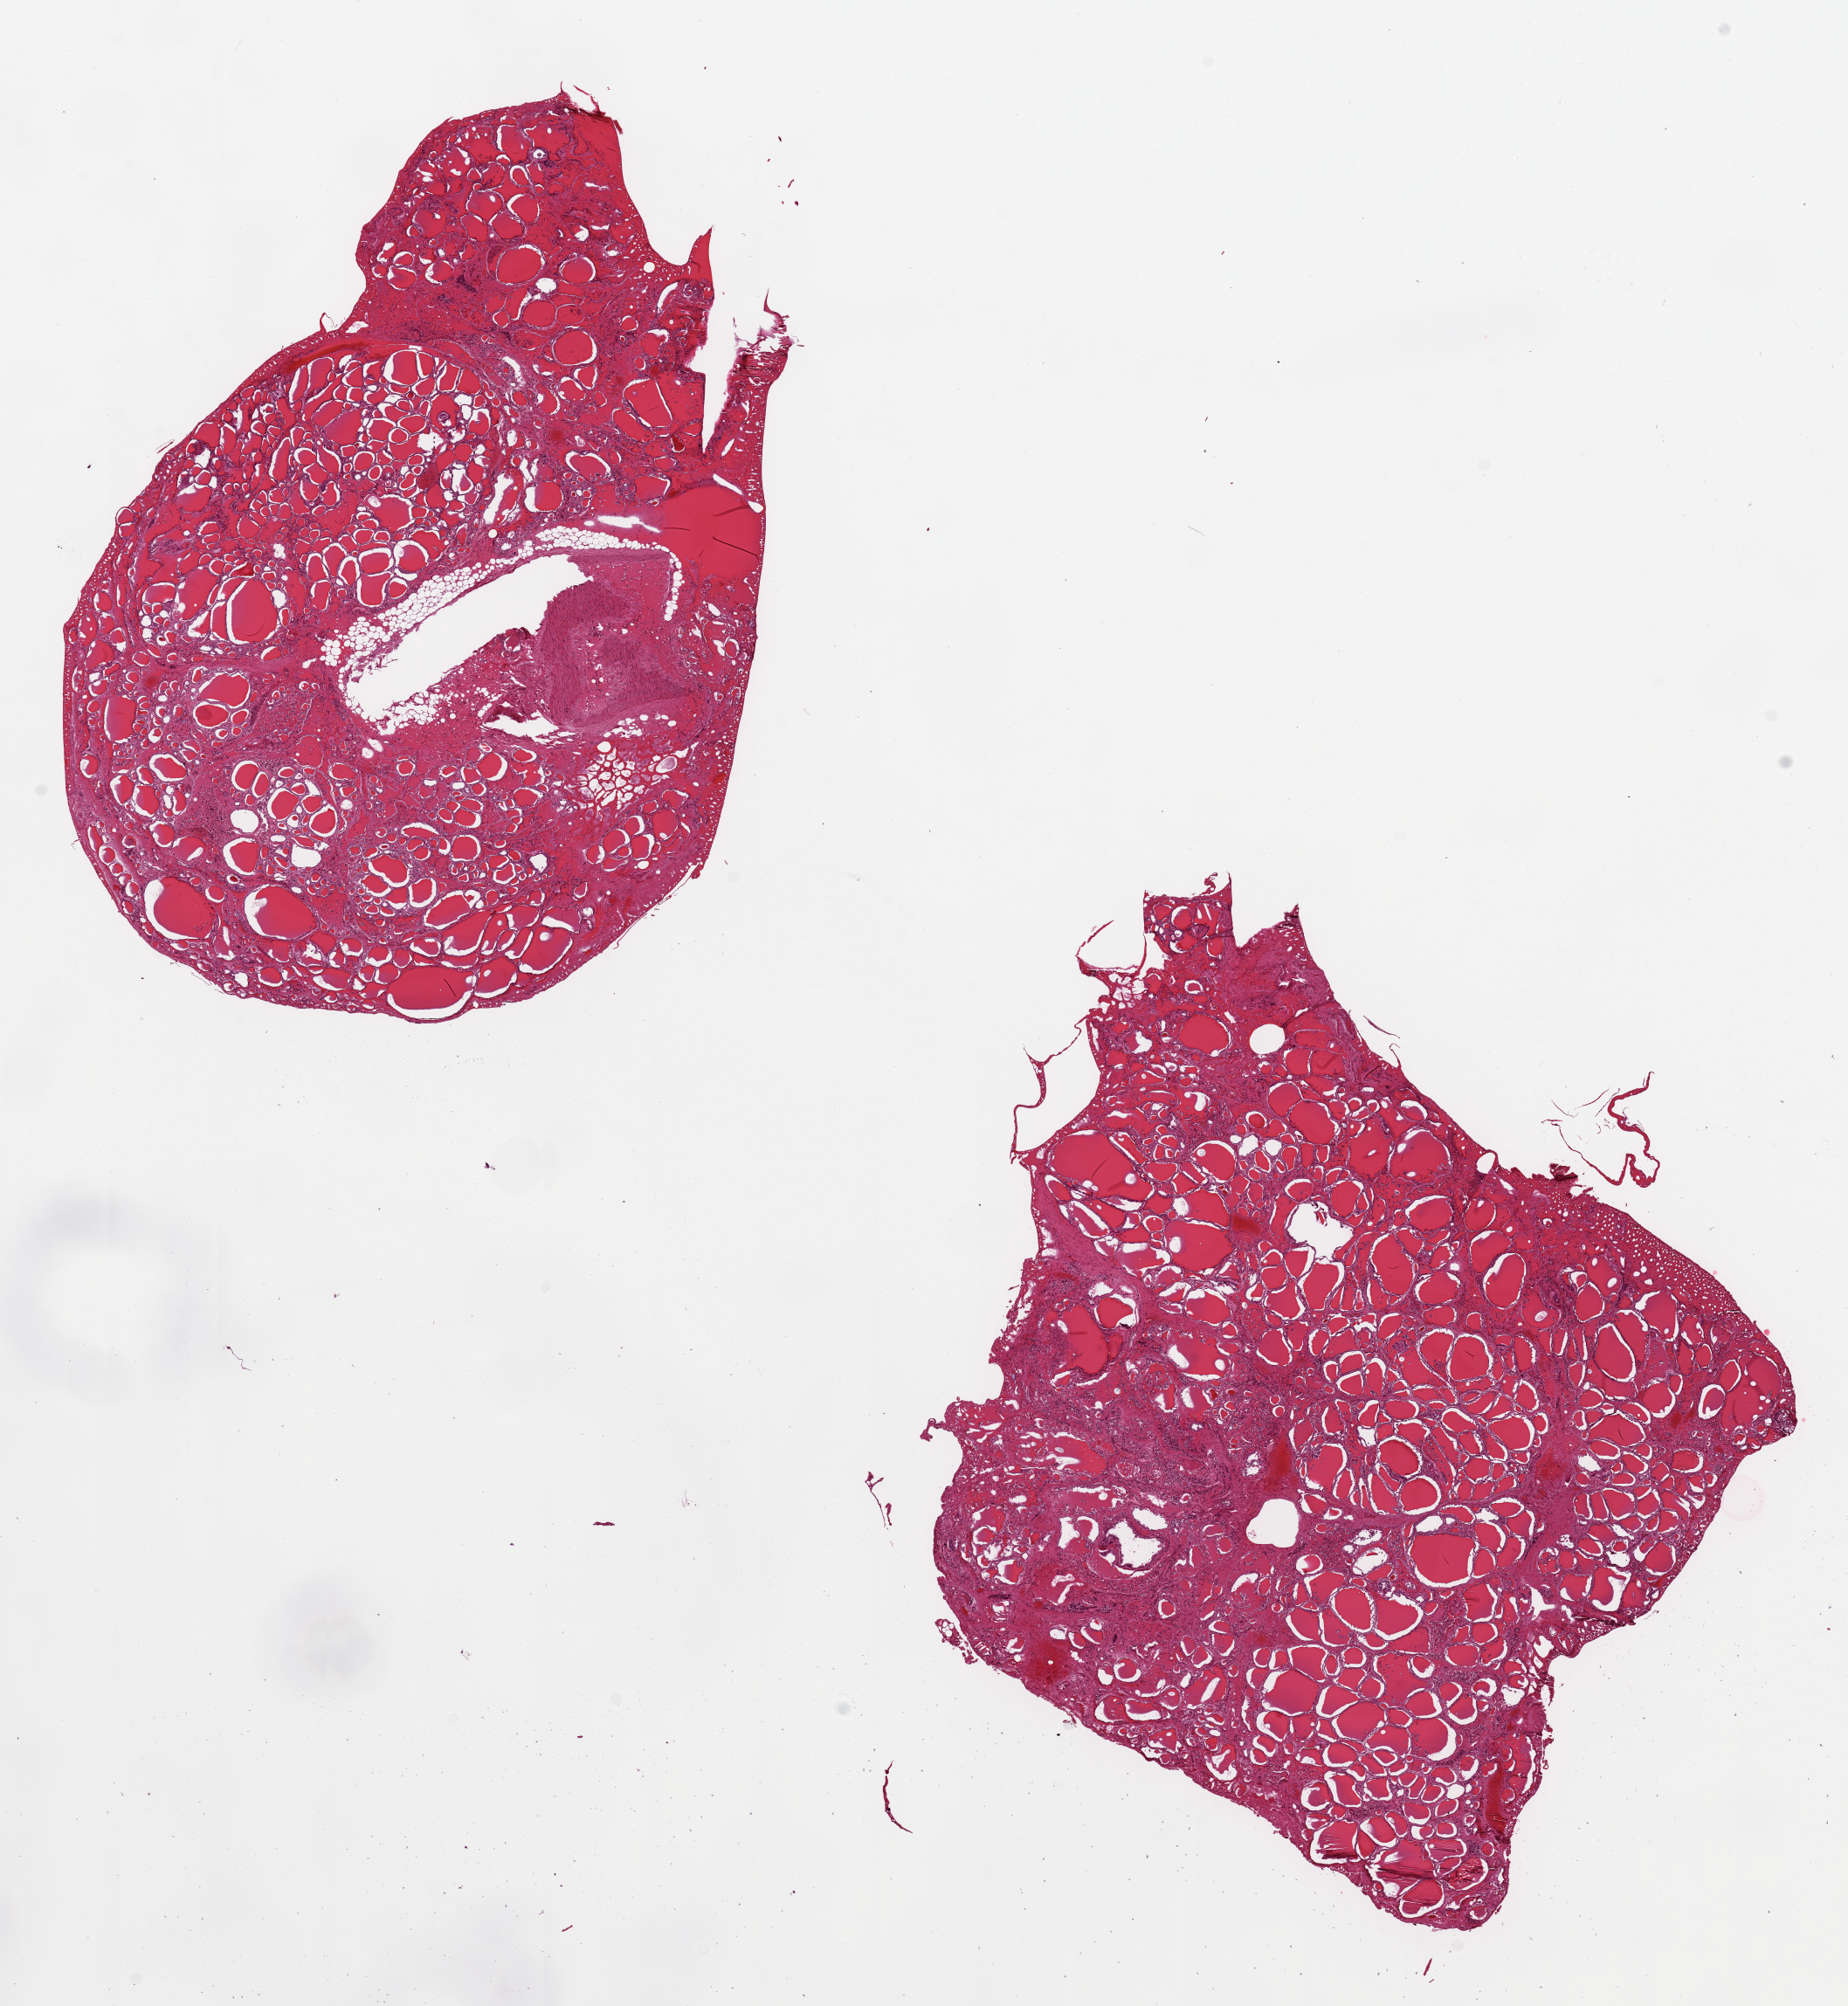
Whole-slide image, H&E stain, whole scanned area (about 16.7 x 18.2 mm) shown as a low-resolution overview. PAXgene-fixed, paraffin-embedded tissue. Section of thyroid (target tissue). Tissue donor sample. Donor: male.
Review note (as recorded): 2 aliquots, ~7x7mm. Patchy thyroiditis/regressive changes. Badly autolyzed.